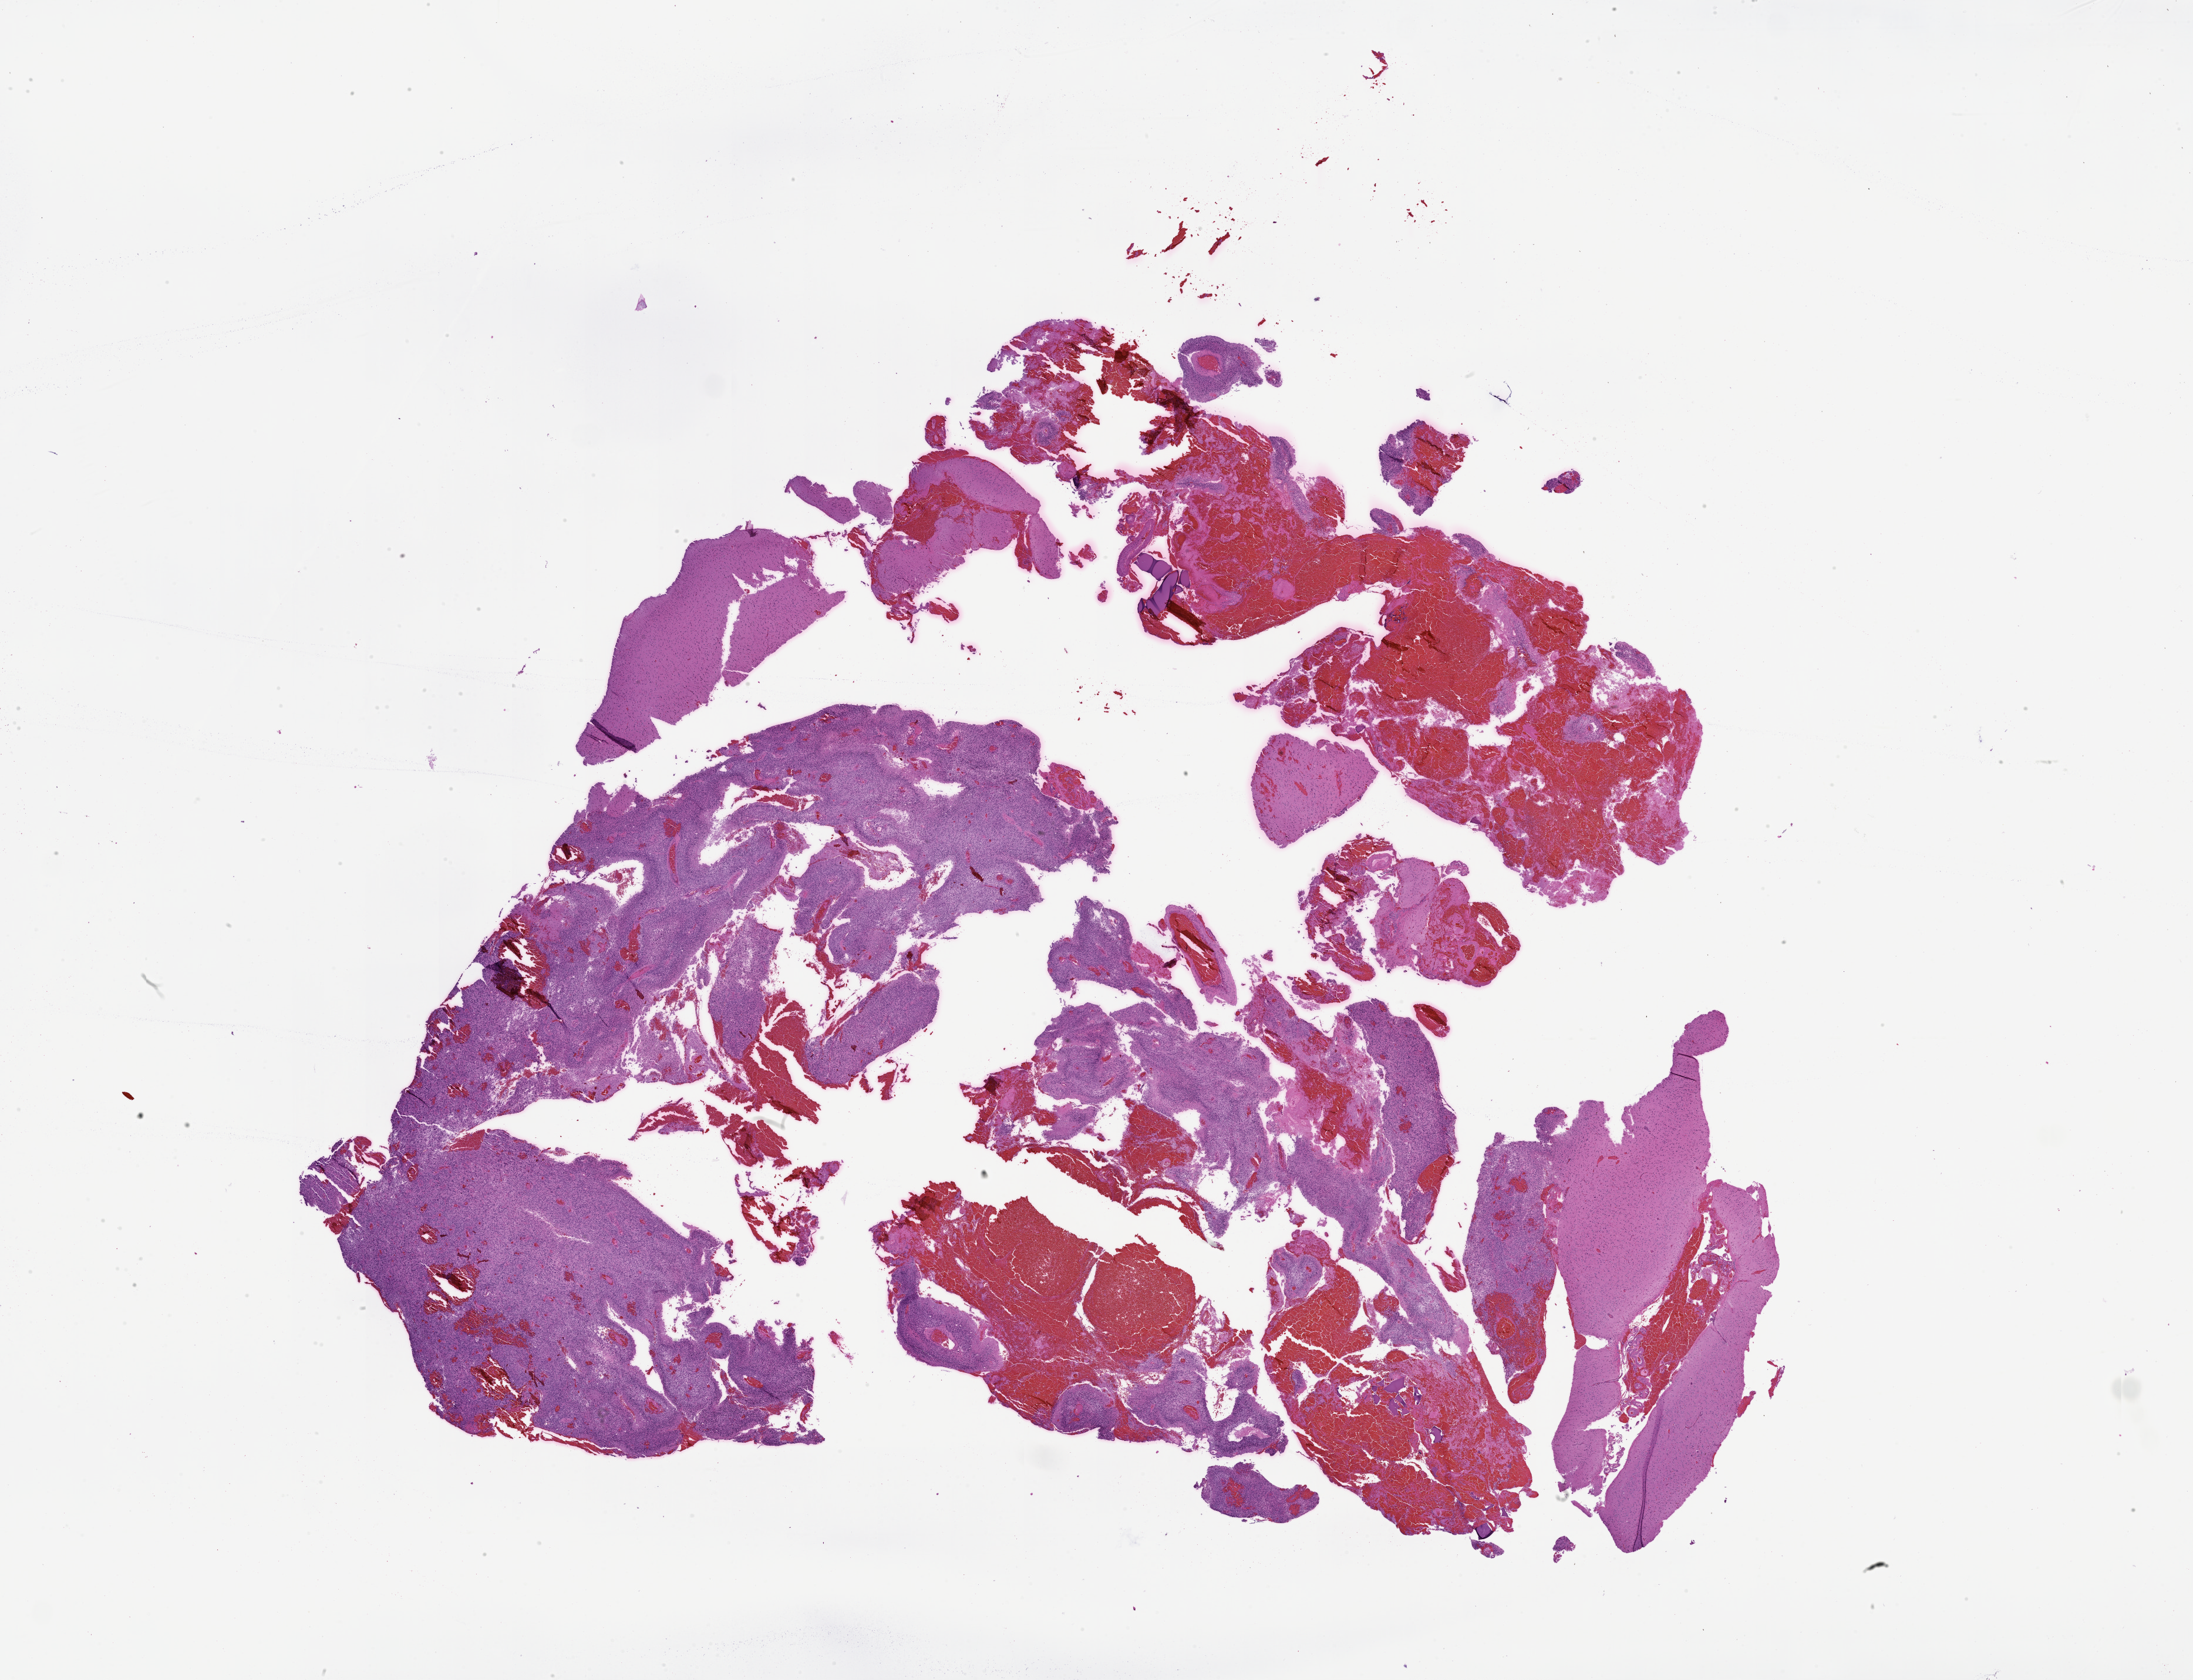
Whole-slide histology image, Hematoxylin and eosin (H&E) stained — whole scanned area (about 30.1 x 23.0 mm) shown as a low-resolution overview. Tumour tissue sample, sampled site: brain. Female, 69 y/o. Pathologist review of this section (percent, as recorded): tumour nuclei 70%, necrosis 7%.
Primary tumour site (as recorded): parietal lobe. Histologic diagnosis: Glioblastoma.